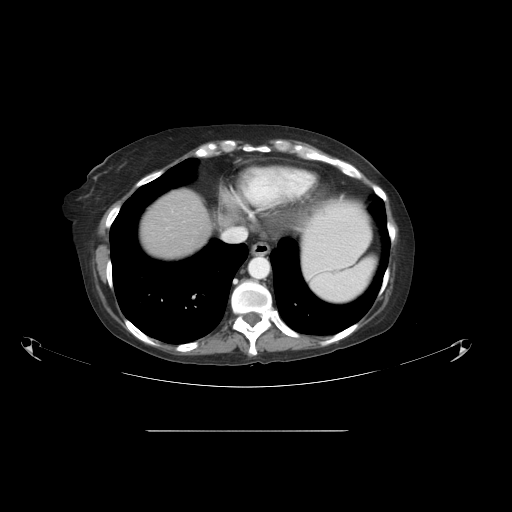
Contrast-enhanced abdominal CT, one axial slice. Position 45 of 51 along the scan axis. Reconstruction kernel STANDARD. 120 kVp. Intravenous contrast given. Soft-tissue window (W 400 / L 40 HU). 5 mm slice thickness. 512 × 512 image matrix, field of view 475 × 475 mm. Female patient, age 48 years. From the clinical record (not read from this slice): diagnosis: colorectal cancer liver metastases, imaged before liver resection; multiple liver metastases: yes; largest metastasis: 1 cm.
Annotated regions visible in this slice (expert manual segmentation):
- liver: box from (x=139, y=190) to (x=213, y=260) px
- planned liver remnant (the part of the liver to remain after resection): (x=139, y=190)–(x=213, y=260)